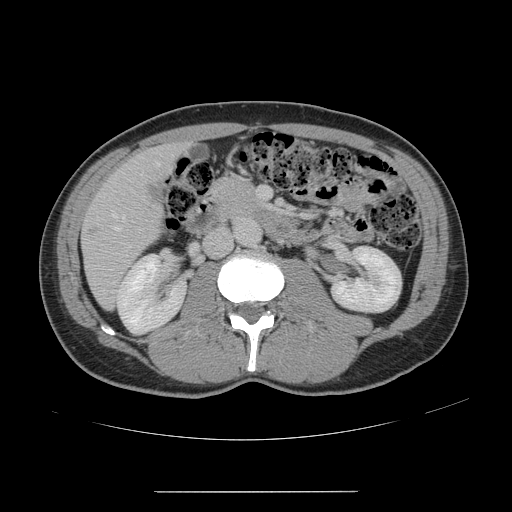
Contrast-enhanced abdominal CT, one axial slice. Slice 55 of 178 in the series (ordered by position). 120 kVp. Intravenous contrast given. Soft-tissue window (W 400 / L 40 HU). 512 × 512 image matrix, field of view 401 × 401 mm. Male patient, age 53 years. From the clinical record (not read from this slice): diagnosis: colorectal cancer liver metastases, imaged before liver resection; multiple liver metastases: yes; largest metastasis: 2.4 cm; disease in both lobes: no.
Outlined on this slice (outlined manually by an expert reader):
- hepatic veins: bounding box (x1, y1, x2, y2) in pixels: (105, 162, 160, 247)
- liver: (83, 145, 182, 307)
- portal vein (with intrahepatic branches): (258, 187, 267, 199)
- liver metastasis: (148, 181, 161, 197)